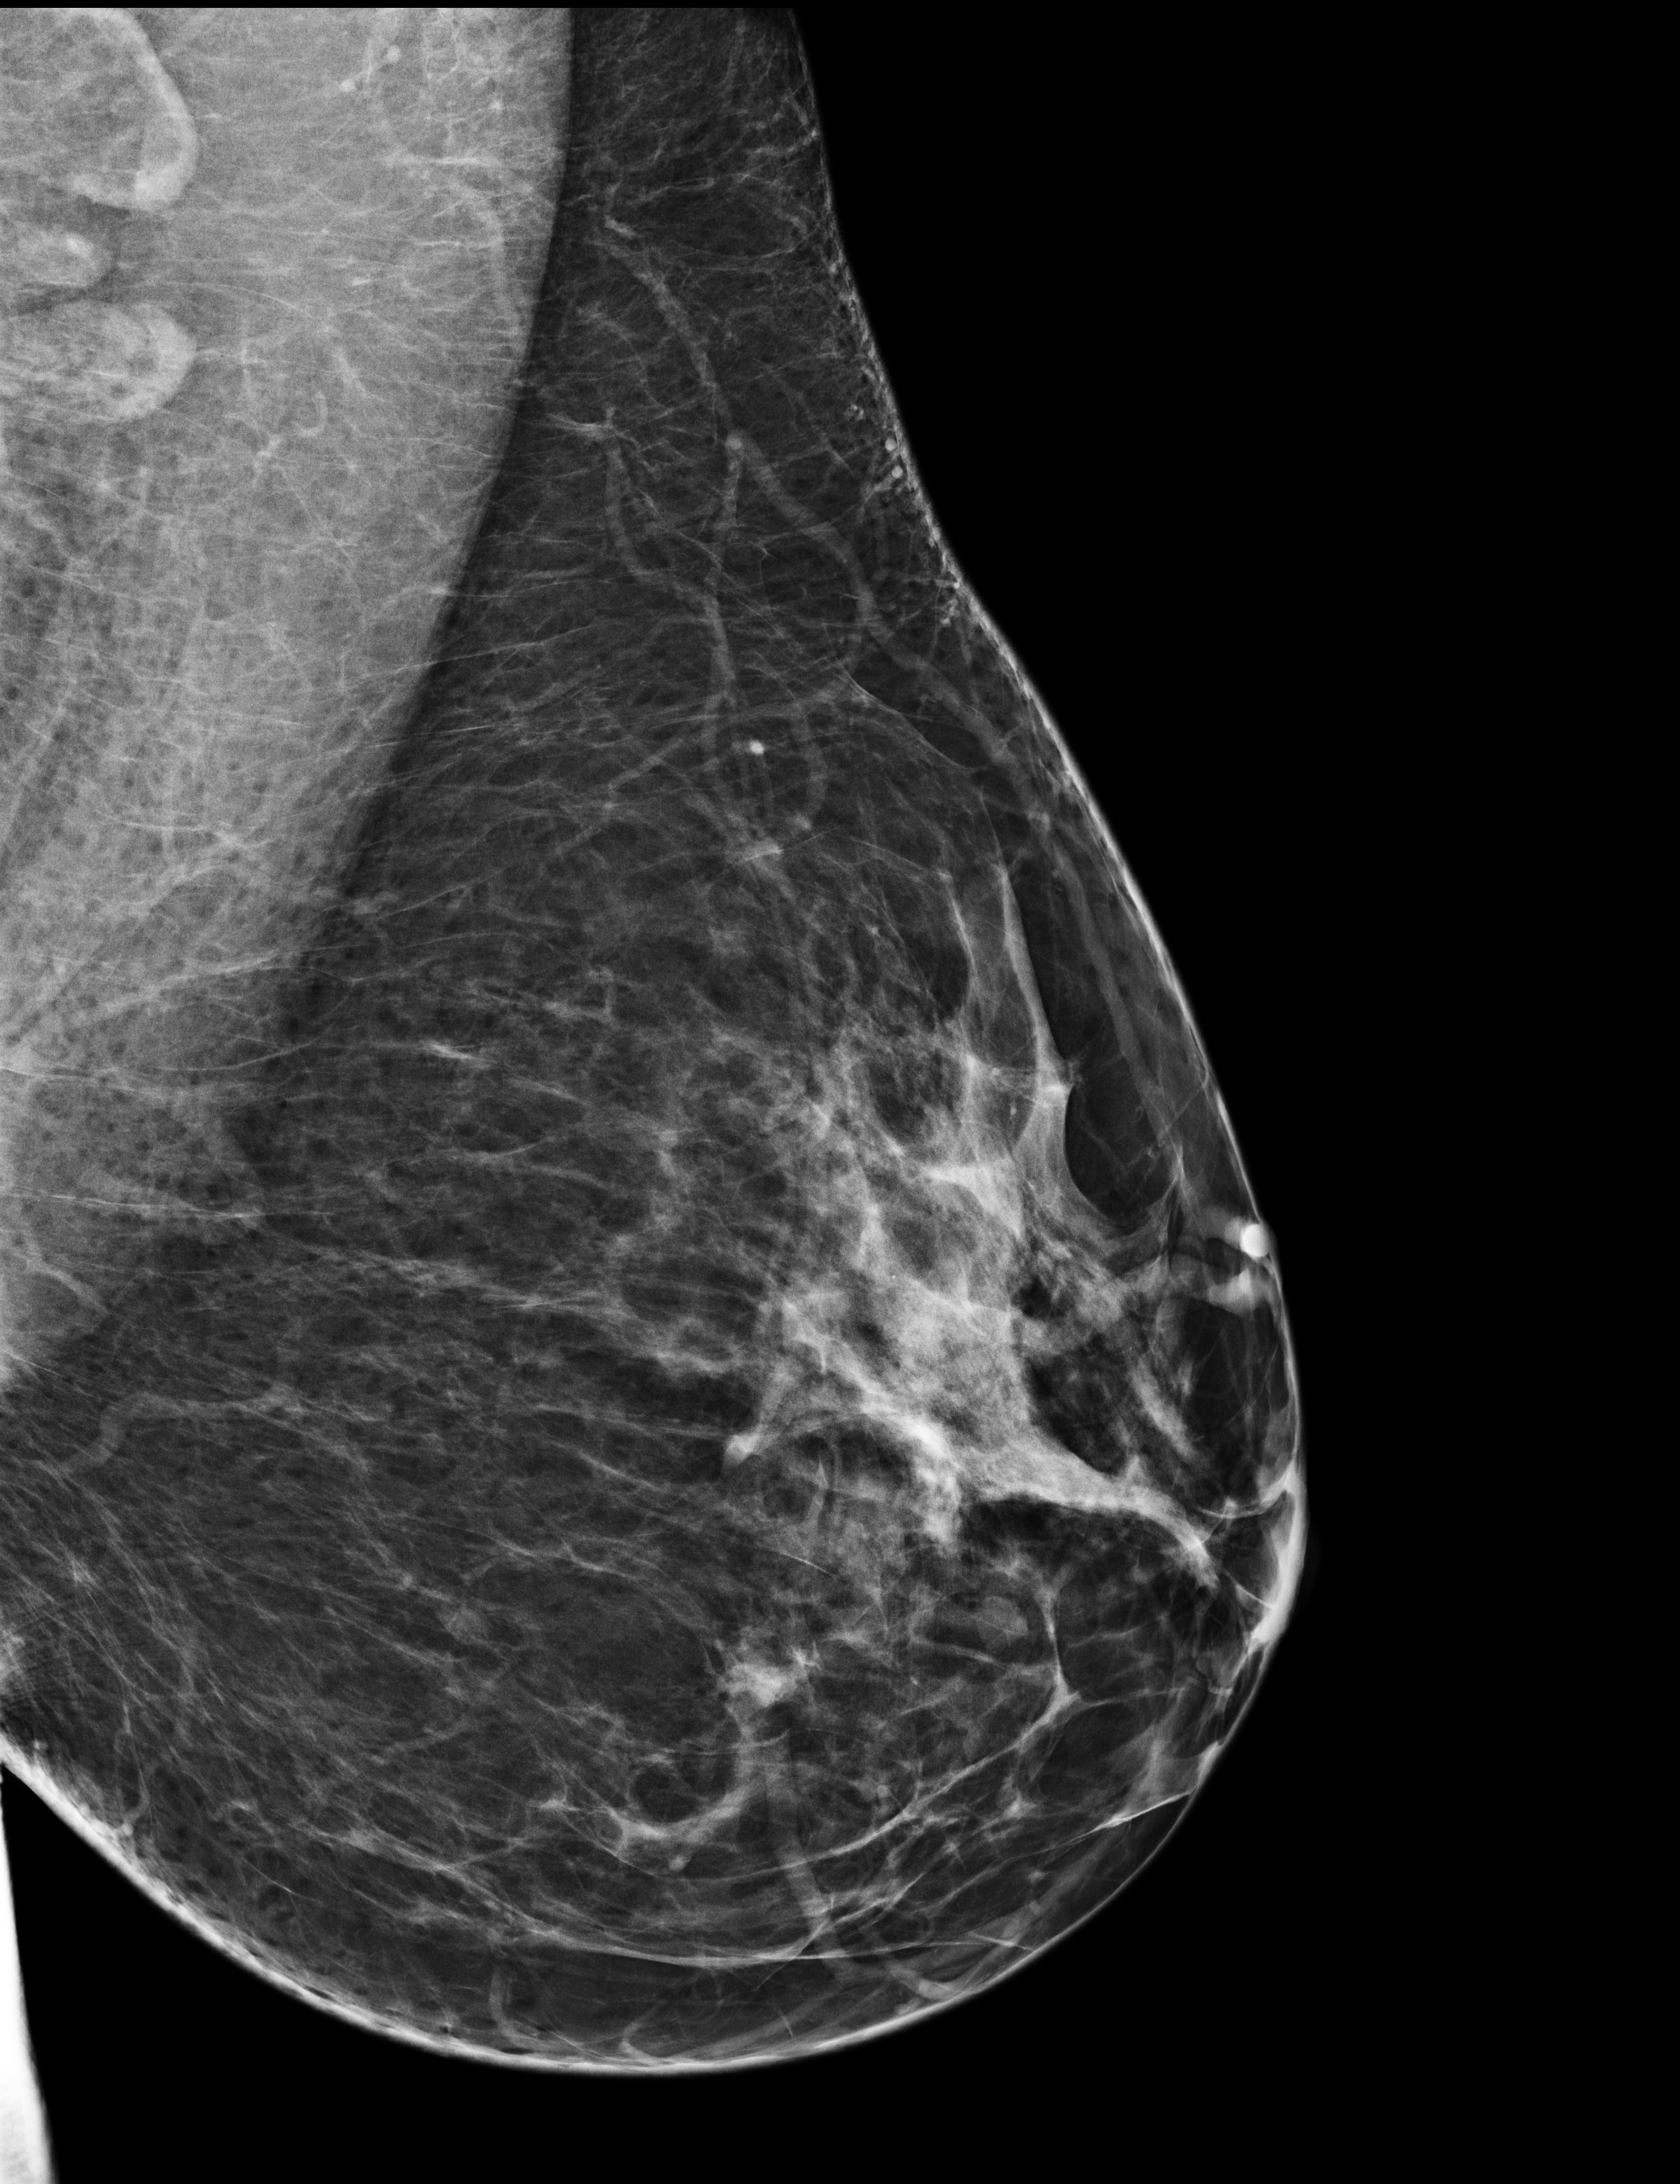
Screening examination; compressed breast thickness 71 mm; system: Selenia Dimensions. Female patient, age 42 years.
Image type: full-field digital mammogram. Breast: left. Projection: mediolateral oblique (MLO) view.